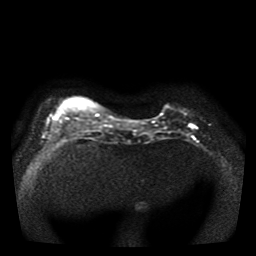
Breast MRI, one axial slice. Slice 10 of 41 in the series (ordered by position). Diffusion-weighted series; image 2 of 4 stored at this slice position (different b-values; order by instance number). 1.5 T. 256 × 256 image matrix. Female patient.
Outlined on this slice (expert manual segmentation):
- tumour on diffusion-weighted imaging: bounding box (x1, y1, x2, y2) in pixels: (190, 125, 194, 128)